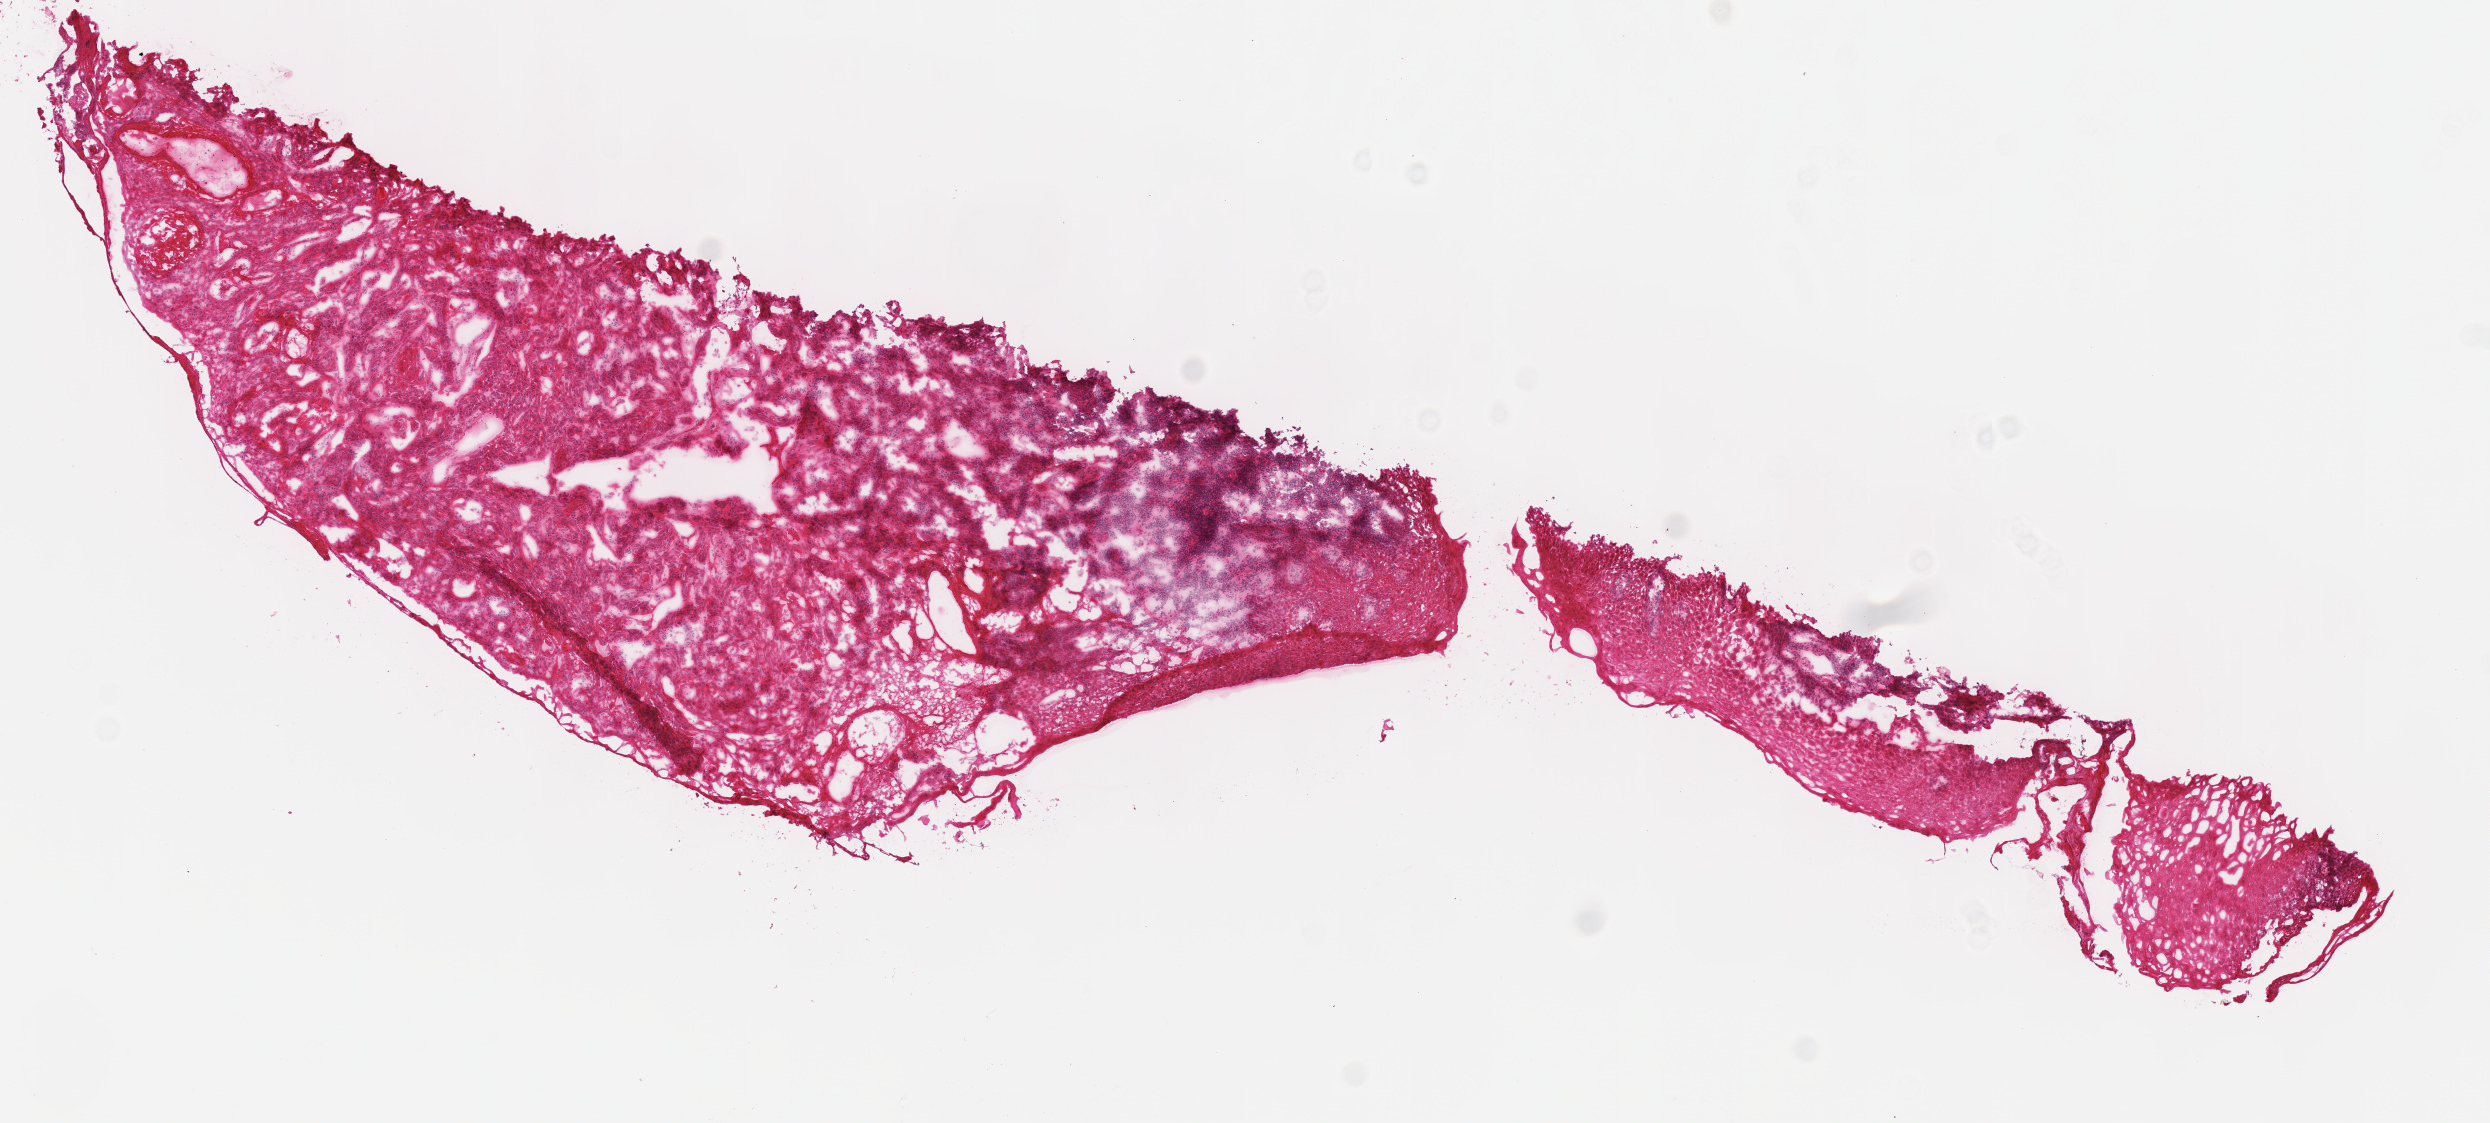
H&E whole-slide image — whole scanned area (about 9.8 x 4.4 mm, acquisition: 40x scan) shown as a low-resolution overview, frozen section from the top of the tissue portion, primary tumour sample from the head and neck. Male, age 63 years at initial diagnosis. Histologic grade: G3 (poorly differentiated). Composition of this section per pathologist review: tumour cells 85%, tumour nuclei 70%, normal cells 0%, stromal cells 15%, necrosis 0%.
Diagnosis: Squamous cell carcinoma, NOS. AJCC pathologic stage: I.